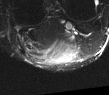
MRI of an extremity soft-tissue mass, one axial slice; slice 12 of 52 in the series (ordered by position); T2-weighted fat-saturated; MR volume resampled by the dataset authors to the PET/CT grid (not the native acquisition matrix); 3.27 mm slice thickness; 109 × 95 image matrix, field of view 106 × 93 mm. Male patient. From the clinical record (not read from this slice): histological type: synovial sarcoma; site of the primary tumour: left poplietal fossa.
Outlined on this slice (expert contour drawn on MRI and transferred to this co-registered scan by the dataset authors):
- gross tumour volume (mass): bounding box (x1, y1, x2, y2) in pixels: (58, 42, 75, 62)